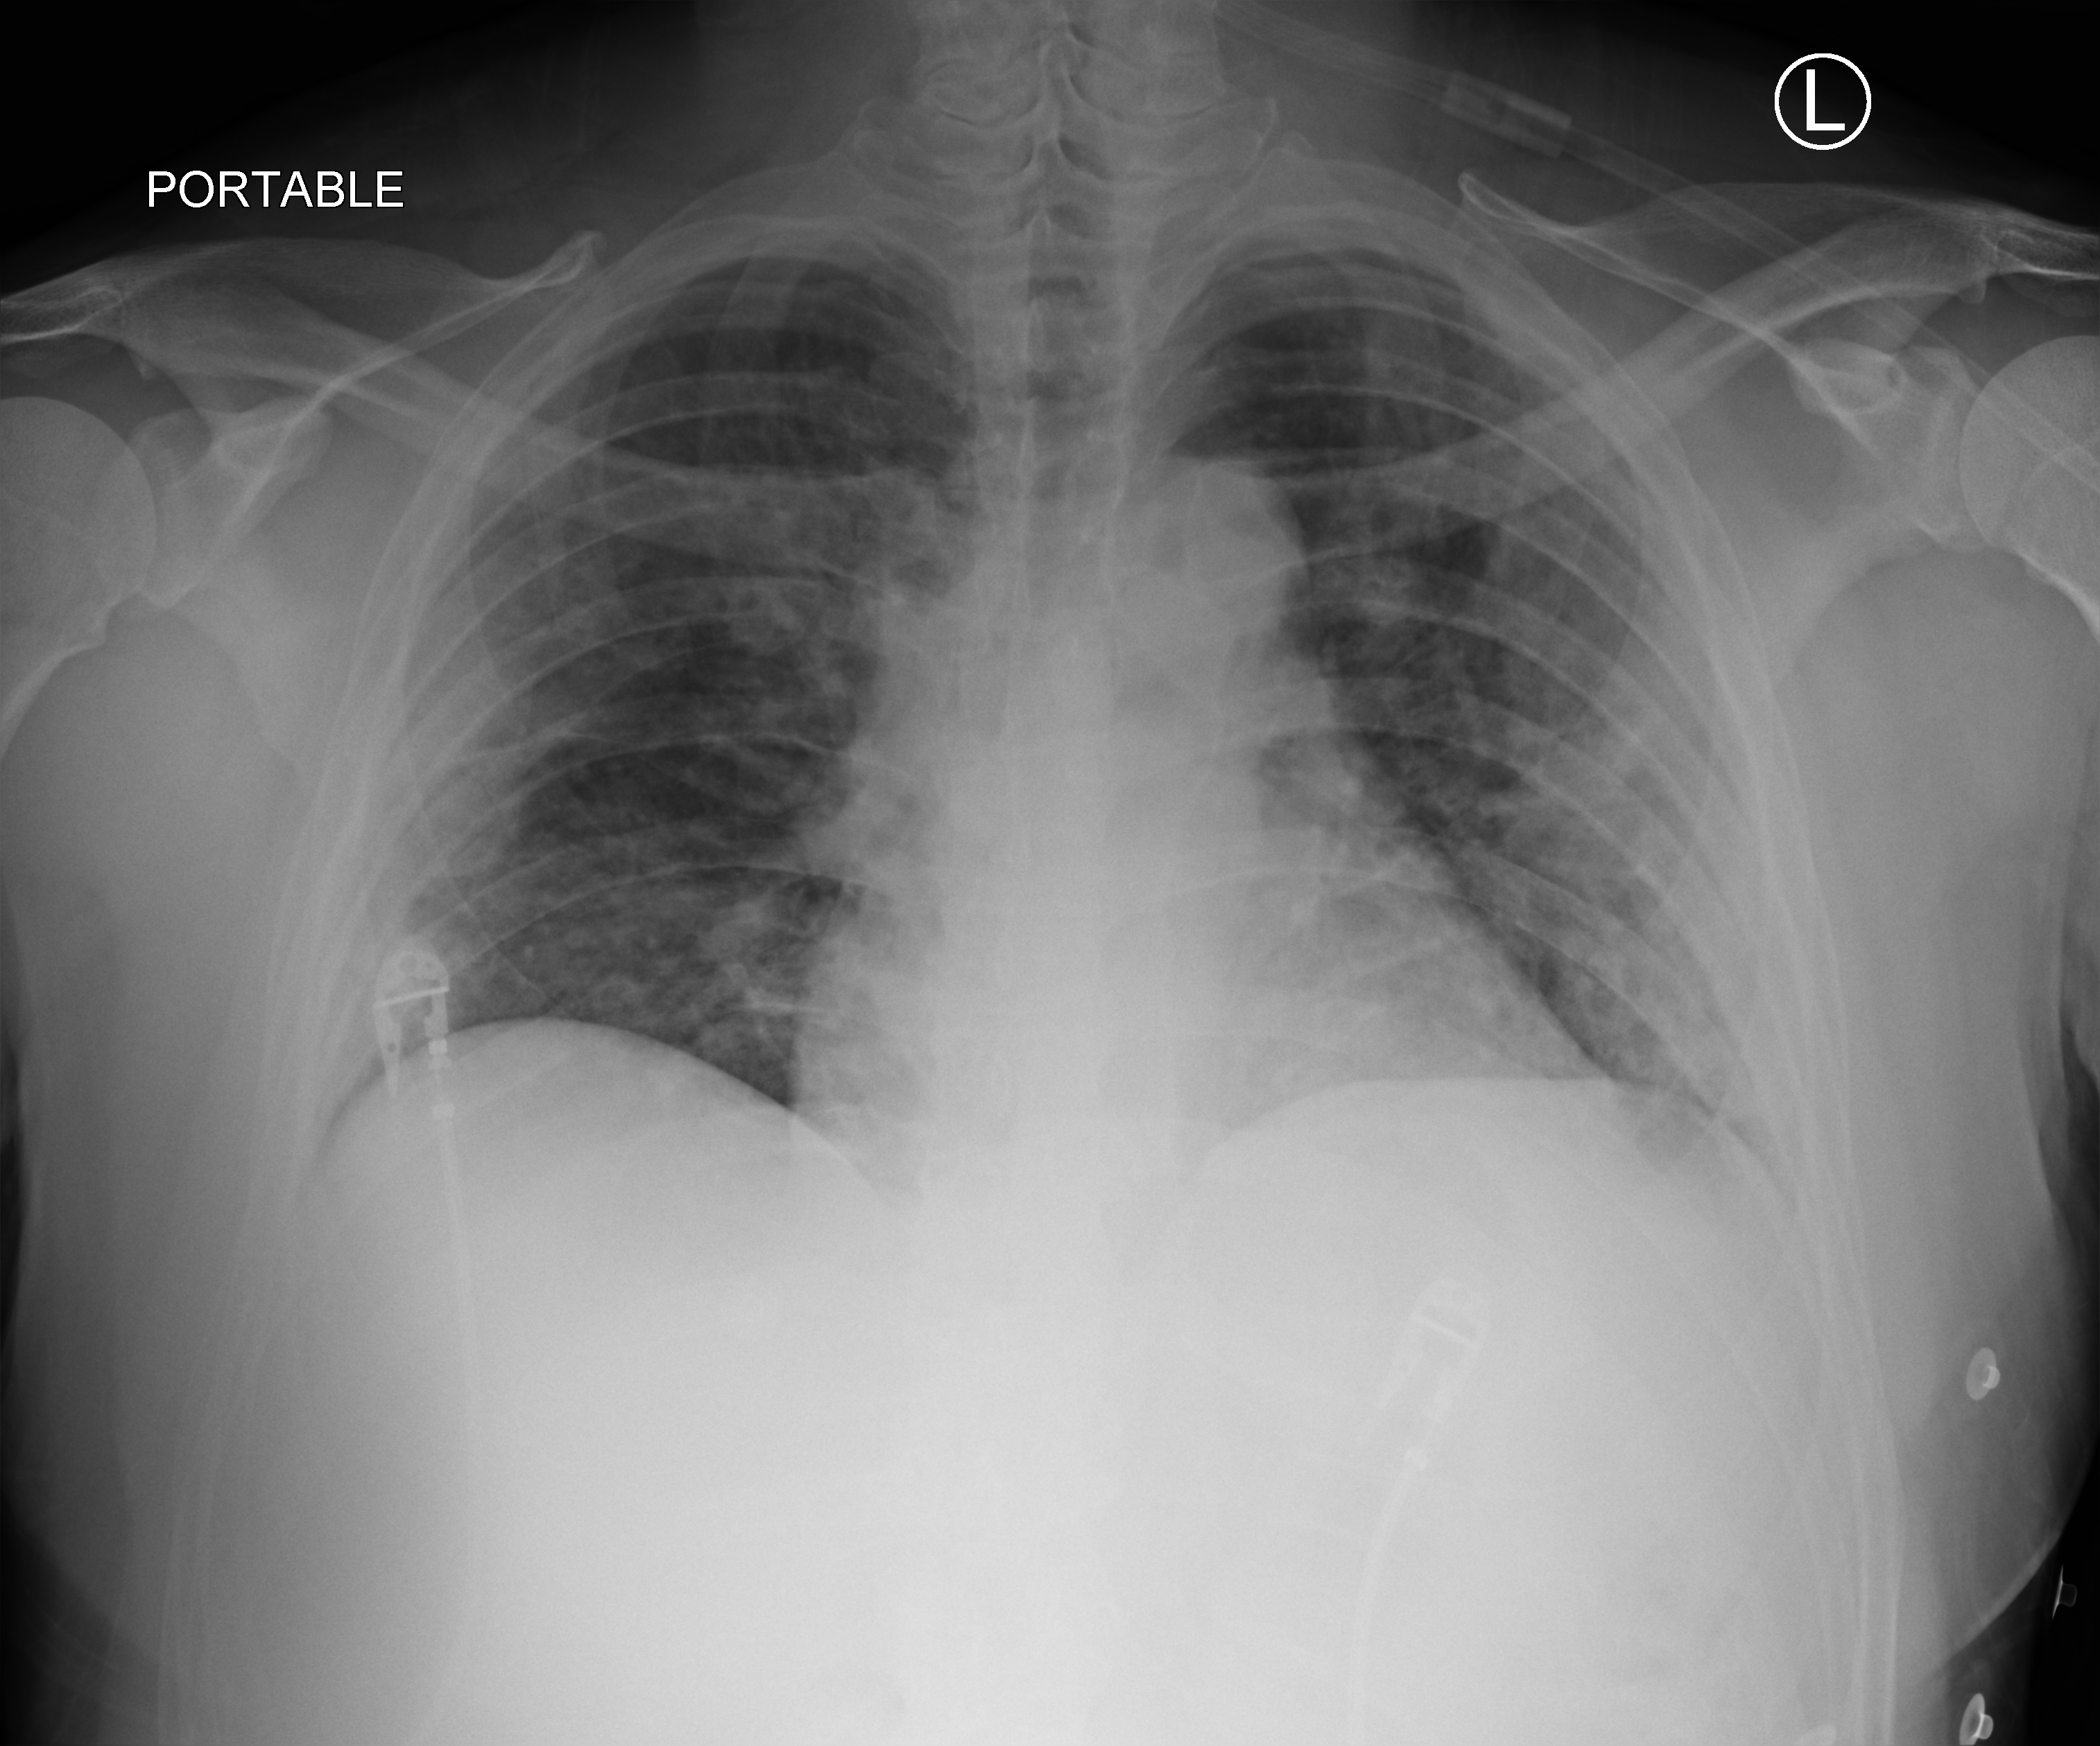
Bedside chest radiograph (computed radiography), anteroposterior (AP) projection. Male patient hospitalised with COVID-19, age 18–59 years.
Hospital-stay facts (about this admission, not read from this image; timing relative to this image not recorded): admitted to intensive care during this hospital stay: yes; mechanically ventilated during this hospital stay: no; hypertension (admission record): no.